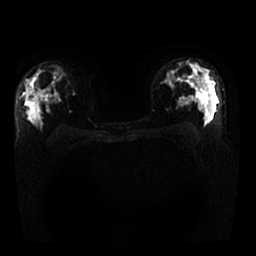
Breast MRI, one axial slice; position 16 of 25 along the scan axis; diffusion-weighted series; image 2 of 4 stored at this slice position (different b-values; order by instance number); 1.5 T; 4 mm slice thickness; 256 × 256 image matrix, field of view 340 × 340 mm. Female patient.
Annotated regions visible in this slice (expert manual segmentation):
- tumour on diffusion-weighted imaging: bounding box <27,86,34,94> (left, top, right, bottom; pixels)